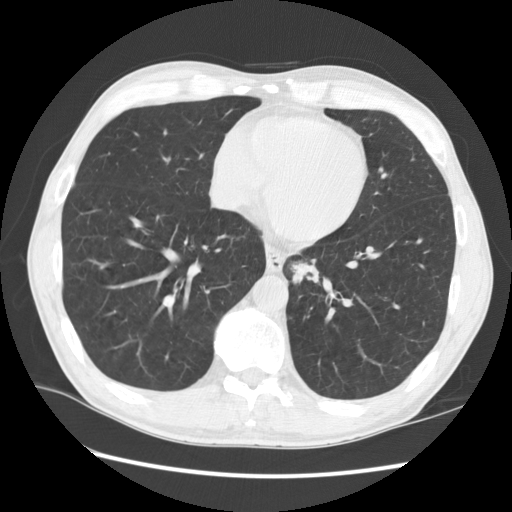
Axial slice from a low-dose chest CT screening exam. First (baseline) screen. Lung window (W 1500 / L -600 HU). 2.5 mm slice thickness. Standard (soft-tissue) reconstruction kernel (STANDARD). Slice 97 of 141 in the series. 512 × 512 image matrix, field of view 360 × 360 mm. Male, age 57 years at enrolment. Current smoker at enrolment.
- Expert reader's lesion annotation, bounding box <268,245,341,309> (left, top, right, bottom; pixels).
- The screening reader recorded 2 non-calcified nodules or masses ≥4 mm on this exam; which of them this box marks is not recorded.
- Participant outcome: lung cancer diagnosed 95 days after this screen — squamous cell carcinoma, NOS, left lower lobe, moderately differentiated (G2), stage IB (AJCC 6th edition), 35 mm at pathology.